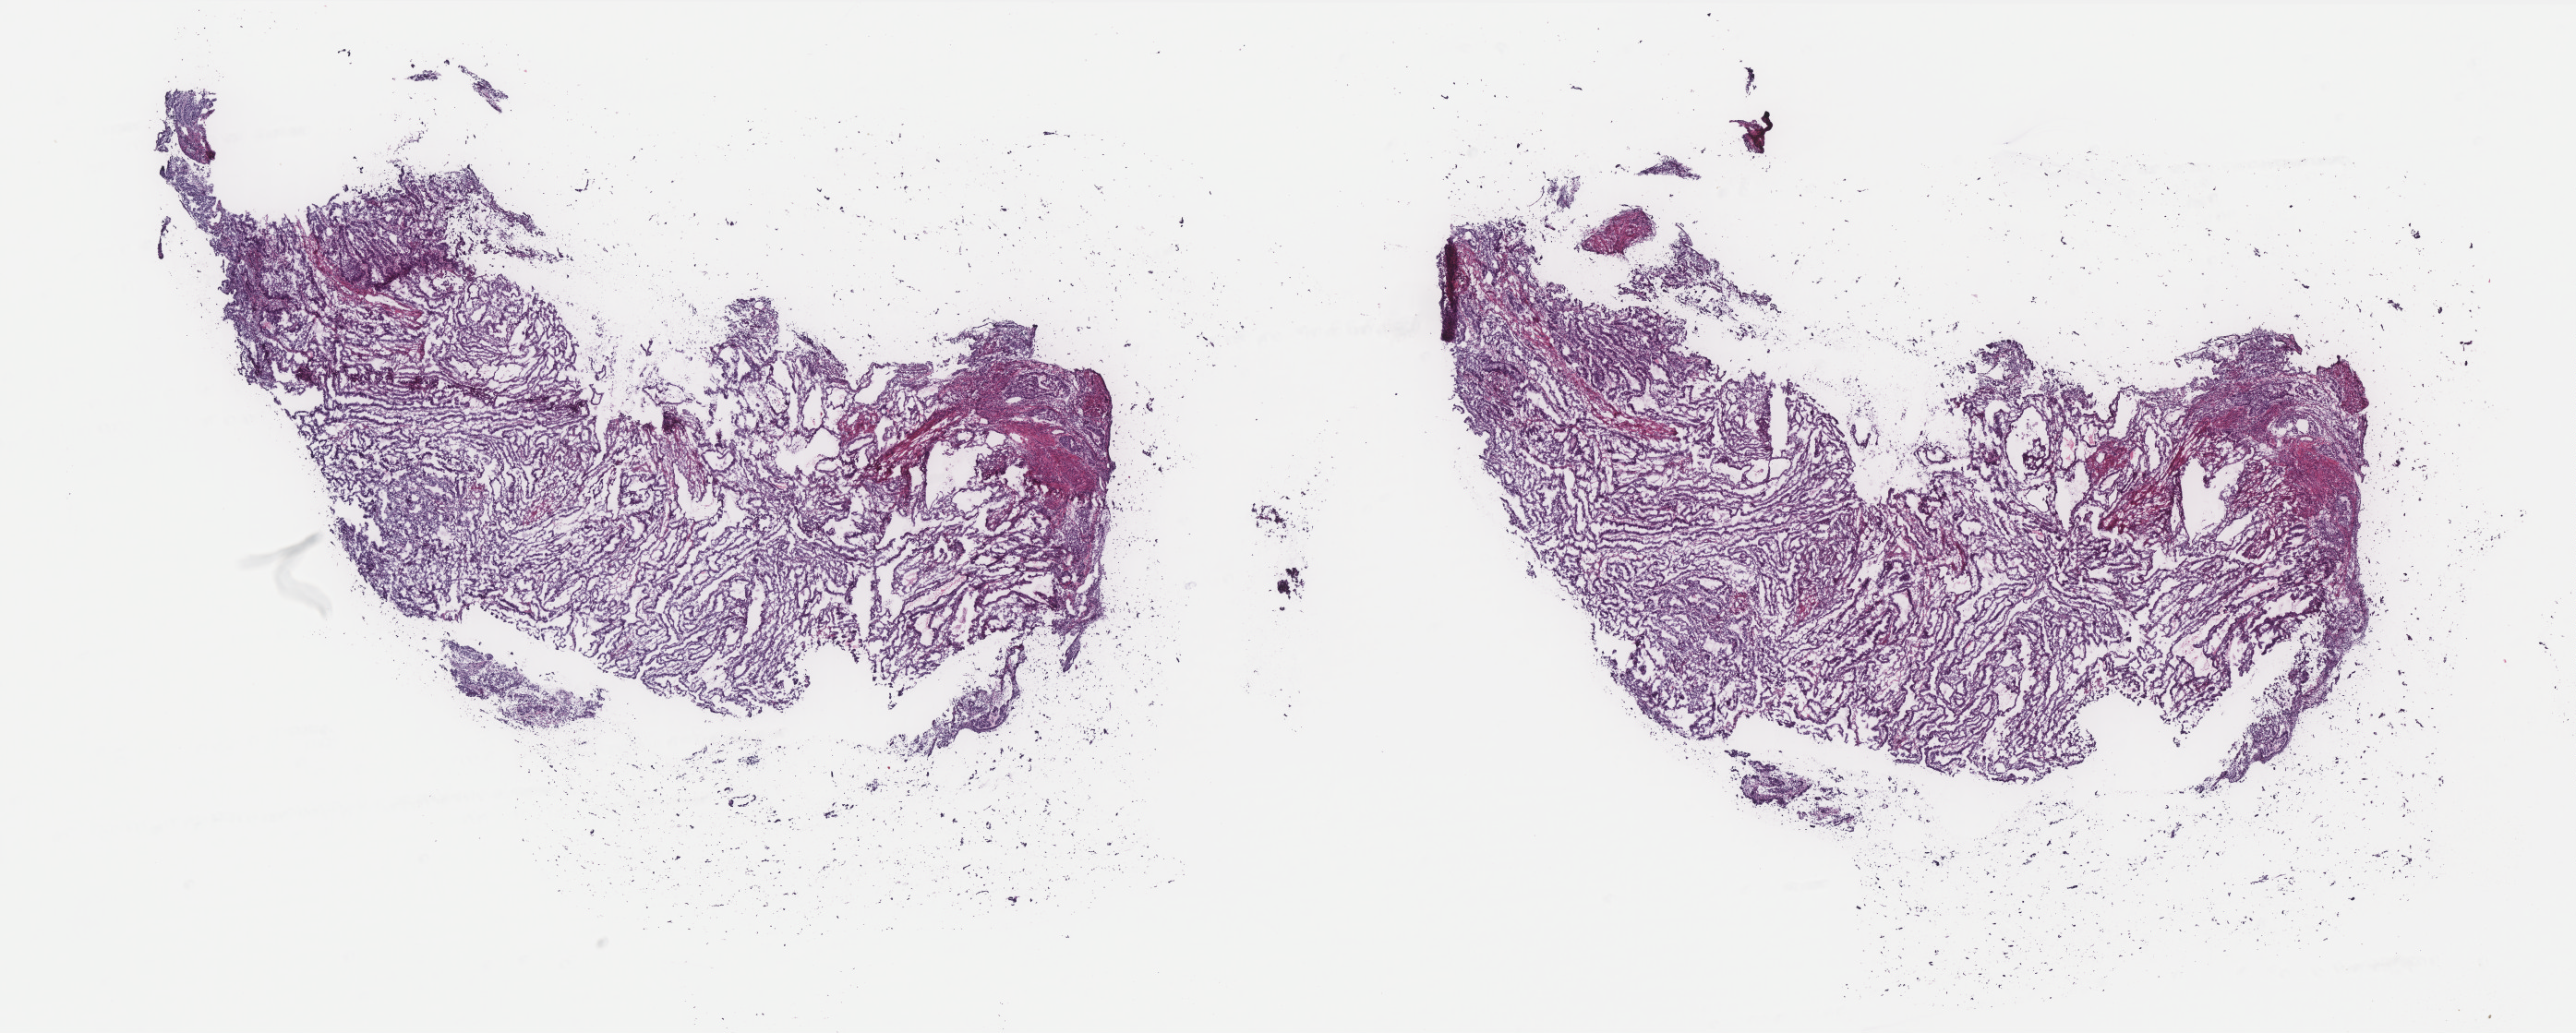
Whole-slide histology image, H&E — low-resolution overview of the scanned area, about 22.4 x 9.0 mm (from a 40x scan), frozen section from the top of the tissue portion, sample: primary tumour, uterus. Patient: female, age at initial diagnosis 57 years. Histologic grade: G1 (well differentiated). Composition of this section per pathologist review: tumour cells 85%, tumour nuclei 85%, normal cells 0%, stromal cells 15%, necrosis 0%. Infiltration values recorded for this section: lymphocyte infiltration 25%, monocyte infiltration 3%, neutrophil infiltration 0%.
Histologic diagnosis: Endometrioid adenocarcinoma, NOS (endometrium). FIGO stage: IIIA.